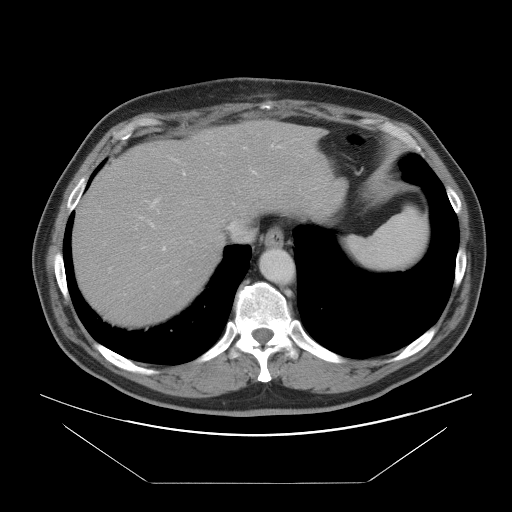
Contrast-enhanced abdominal CT, one axial slice; position 76 of 97 along the scan axis; 120 kVp; intravenous contrast given; soft-tissue window (W 400 / L 40 HU); 512 × 512 image matrix. Male patient, age 62 years. Case-level facts recorded for this patient, not image findings: diagnosis: colorectal cancer liver metastases, imaged before liver resection; multiple liver metastases: no; largest metastasis: 7 cm; disease in both lobes: yes.
Annotated regions visible in this slice (outlined manually by an expert reader):
- hepatic veins: box from (x=228, y=155) to (x=301, y=241) px
- liver: (x=74, y=123)–(x=331, y=322)
- planned liver remnant (the part of the liver to remain after resection): (x=74, y=172)–(x=227, y=322)
- portal vein (with intrahepatic branches): (x=140, y=144)–(x=281, y=250)